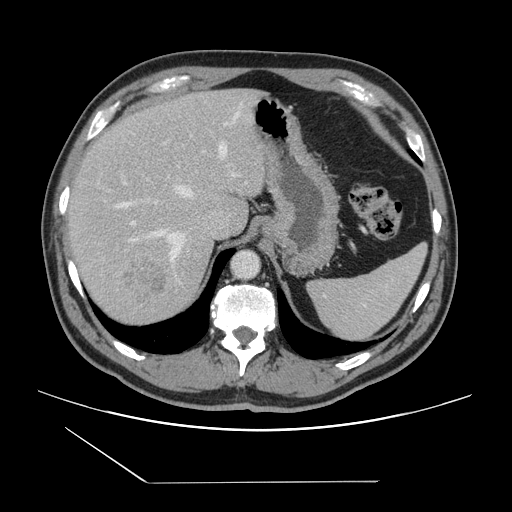
Contrast-enhanced abdominal CT, one axial slice. Slice 111 of 157 in the series (ordered by position). Soft-tissue window (W 400 / L 40 HU). 512 × 512 image matrix. Male patient, age 61 years. Case-level facts recorded for this patient, not image findings: diagnosis: colorectal cancer liver metastases, imaged before liver resection; multiple liver metastases: yes; largest metastasis: 5.5 cm; disease in both lobes: yes.
Structures marked on this image (outlined manually by an expert reader):
- hepatic veins: bounding box [x1, y1, x2, y2] px = [120, 113, 239, 279]
- liver: [68, 90, 266, 327]
- planned liver remnant (the part of the liver to remain after resection): [67, 89, 236, 231]
- portal vein (with intrahepatic branches): [124, 142, 238, 225]
- liver metastasis: [116, 252, 176, 310]